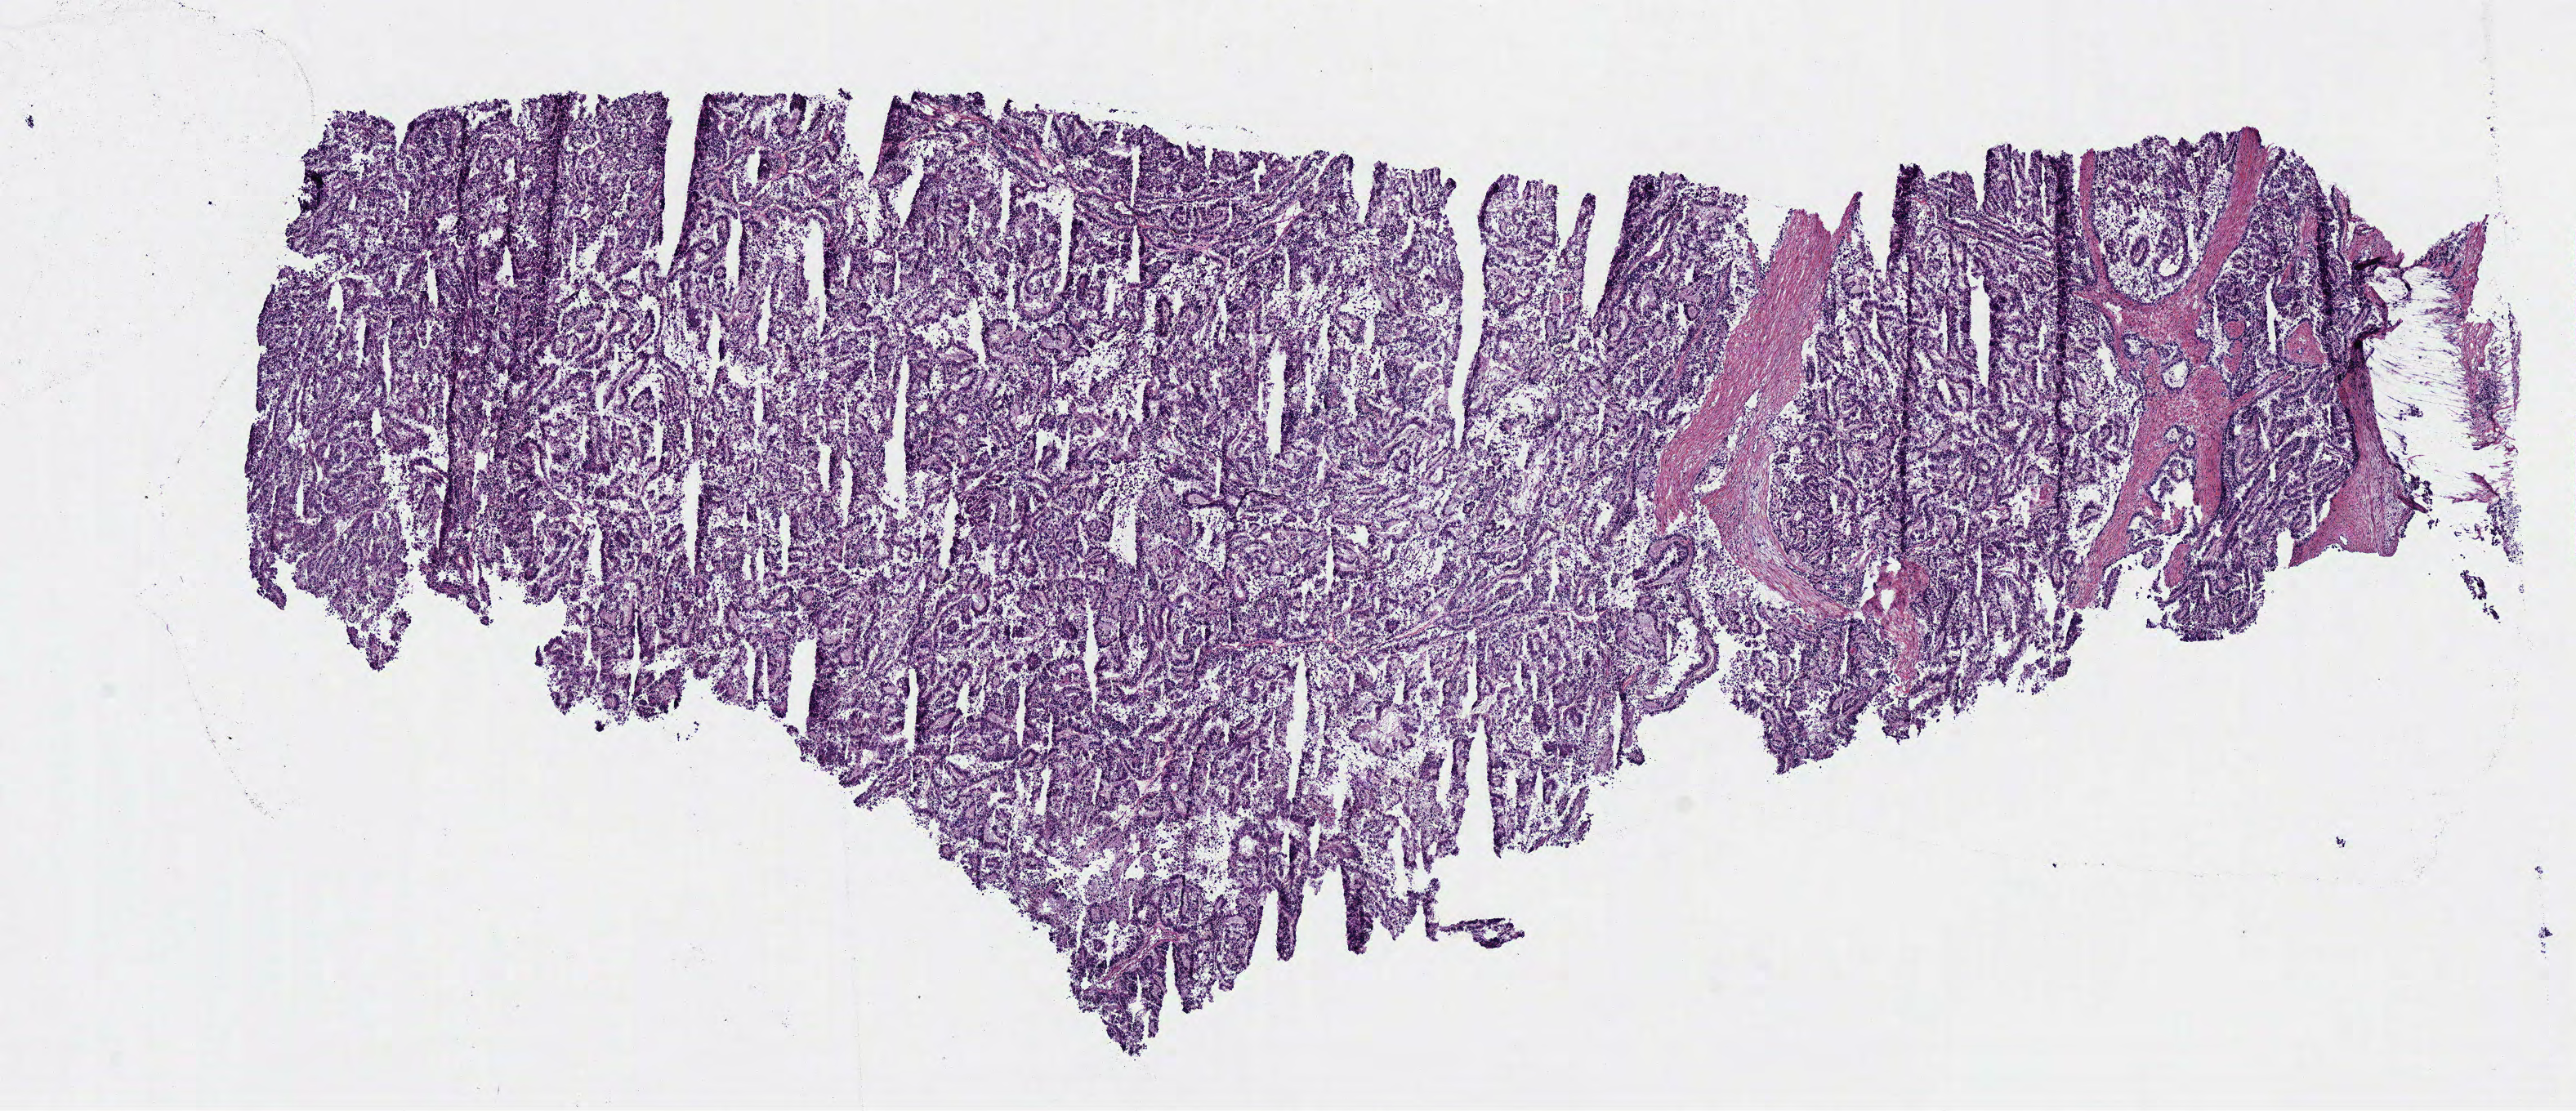
Digitized Hematoxylin and eosin (H&E) stained tissue section (whole slide) — low-resolution overview of the scanned area, about 12.4 x 5.4 mm (acquisition: 40x scan). Frozen section from the bottom of the tissue portion. Kidney, primary tumour sample. Male, age 31 years at initial diagnosis. Pathologist review of this section (percent, as recorded): tumour cells 90%, tumour nuclei 80%, normal cells 0%, stromal cells 10%, necrosis 0%.
AJCC pathologic stage: III (6th edition). Pathologic diagnosis: Papillary adenocarcinoma, NOS. Lymph nodes positive (case pathology): 0 of 1 examined.